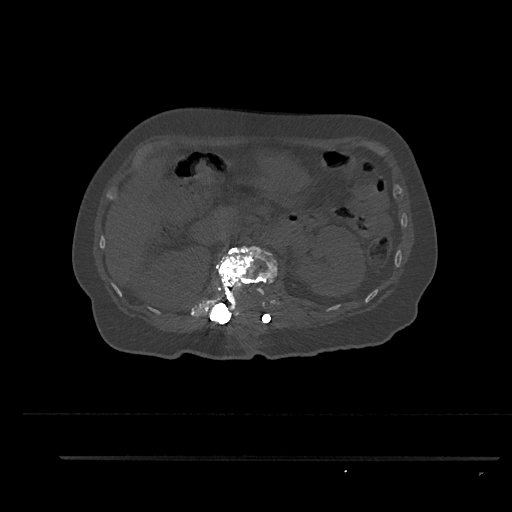
CT including the spine, one axial slice; position 211 of 797 along the scan axis; reconstruction kernel Br40s/3; 120 kVp; bone window (W 1800 / L 400 HU); 0.5 mm slice thickness; 512 × 512 image matrix, field of view 408 × 408 mm. Patient: female, 44 years. Case-level facts recorded for this patient, not image findings: primary cancer: renal; vertebrae with lytic lesions (as recorded): L1.
Structures marked on this image (semi-automatically segmented with operator editing):
- L1 vertebra: bounding box (x1, y1, x2, y2) in pixels: (204, 246, 278, 323)